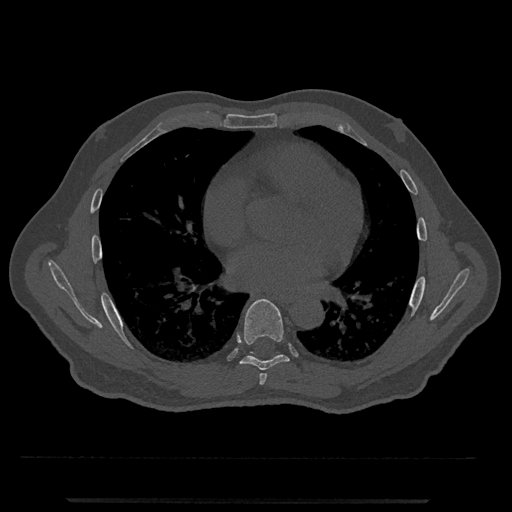
CT including the spine, one axial slice. Slice 679 of 797 in the series (ordered by position). Reconstruction kernel Br40s/3. 120 kVp. Bone window (W 1800 / L 400 HU). 0.5 mm slice thickness. 512 × 512 image matrix, field of view 419 × 419 mm. Patient: male, 63 years. Case-level facts recorded for this patient, not image findings: primary cancer: prostate.
Outlined on this slice (semi-automatic segmentation, software-assisted and operator-edited):
- T6 vertebra: box from (x=259, y=373) to (x=267, y=385) px
- T7 vertebra: (x=237, y=299)–(x=289, y=371)
- T8 vertebra: (x=250, y=352)–(x=254, y=354)